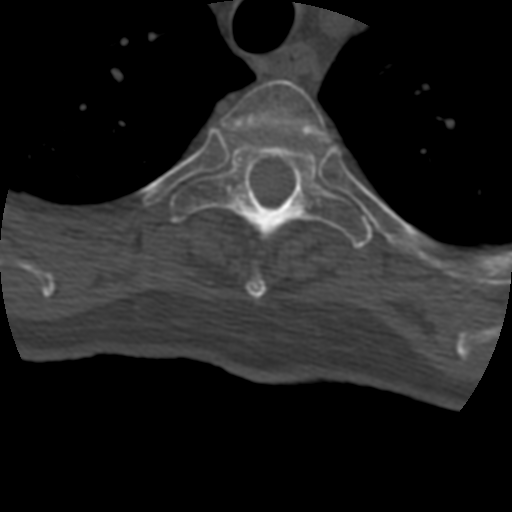
CT including the spine, one axial slice. Position 341 of 399 along the scan axis. Reconstruction kernel STANDARD. 120 kVp. Bone window (W 1800 / L 400 HU). 512 × 512 image matrix, field of view 160 × 160 mm. Patient age 69 years. From the clinical record (not read from this slice): primary cancer: prostate.
Structures marked on this image (semi-automatically segmented with operator editing):
- T3 vertebra: box from (x=222, y=80) to (x=328, y=299) px
- T4 vertebra: (x=171, y=139)–(x=374, y=248)